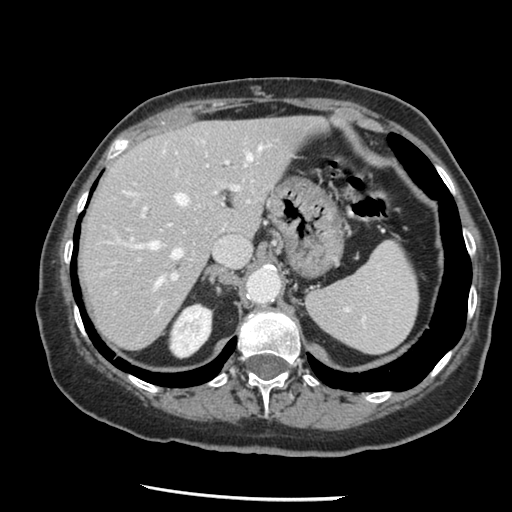
Contrast-enhanced abdominal CT, one axial slice; position 97 of 148 along the scan axis; 120 kVp; soft-tissue window (W 400 / L 40 HU); 2.5 mm slice thickness; 512 × 512 image matrix. Female patient, age 85 years. From the clinical record (not read from this slice): diagnosis: colorectal cancer liver metastases, imaged before liver resection; multiple liver metastases: no; largest metastasis: 0.9 cm; disease in both lobes: no.
Outlined on this slice (outlined manually by an expert reader):
- hepatic veins: box from (x=122, y=142) to (x=272, y=288) px
- liver: (x=81, y=118)–(x=318, y=349)
- planned liver remnant (the part of the liver to remain after resection): (x=81, y=118)–(x=318, y=349)
- portal vein (with intrahepatic branches): (x=130, y=159)–(x=240, y=309)